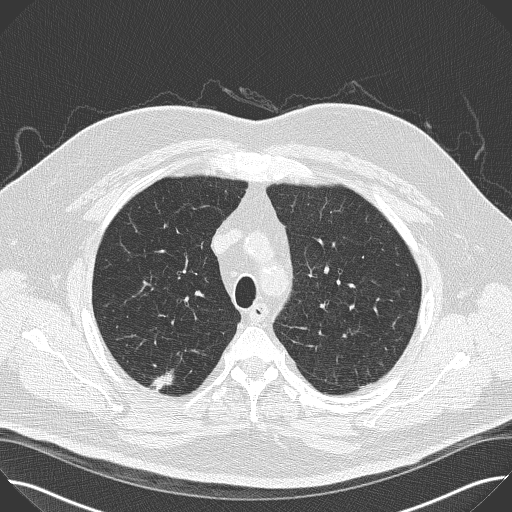
Low-dose screening chest CT, one axial slice. Position 124 of 160 along the scan axis. Lung window (W 1500 / L -600 HU). 512 × 512 image matrix, field of view 380 × 380 mm.
Structures marked on this image (expert manual segmentation):
- lesion 1 (tumor, upper lobe of right lung): bounding box <152,370,174,392> (left, top, right, bottom; pixels)